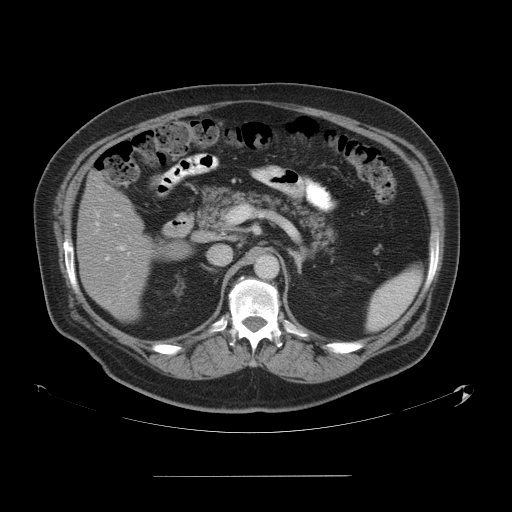
Contrast-enhanced abdominal CT, one axial slice. Position 28 of 58 along the scan axis. Intravenous contrast given. Soft-tissue window (W 400 / L 40 HU). 5 mm slice thickness. 512 × 512 image matrix, field of view 480 × 480 mm. Male patient, age 63 years. Case-level facts recorded for this patient, not image findings: diagnosis: colorectal cancer liver metastases, imaged before liver resection; multiple liver metastases: no; largest metastasis: 4.2 cm; disease in both lobes: no.
Structures marked on this image (outlined manually by an expert reader):
- hepatic veins: bounding box <109,253,129,302> (left, top, right, bottom; pixels)
- liver: <77,175,186,320>
- planned liver remnant (the part of the liver to remain after resection): <78,177,187,320>
- portal vein (with intrahepatic branches): <96,223,124,260>